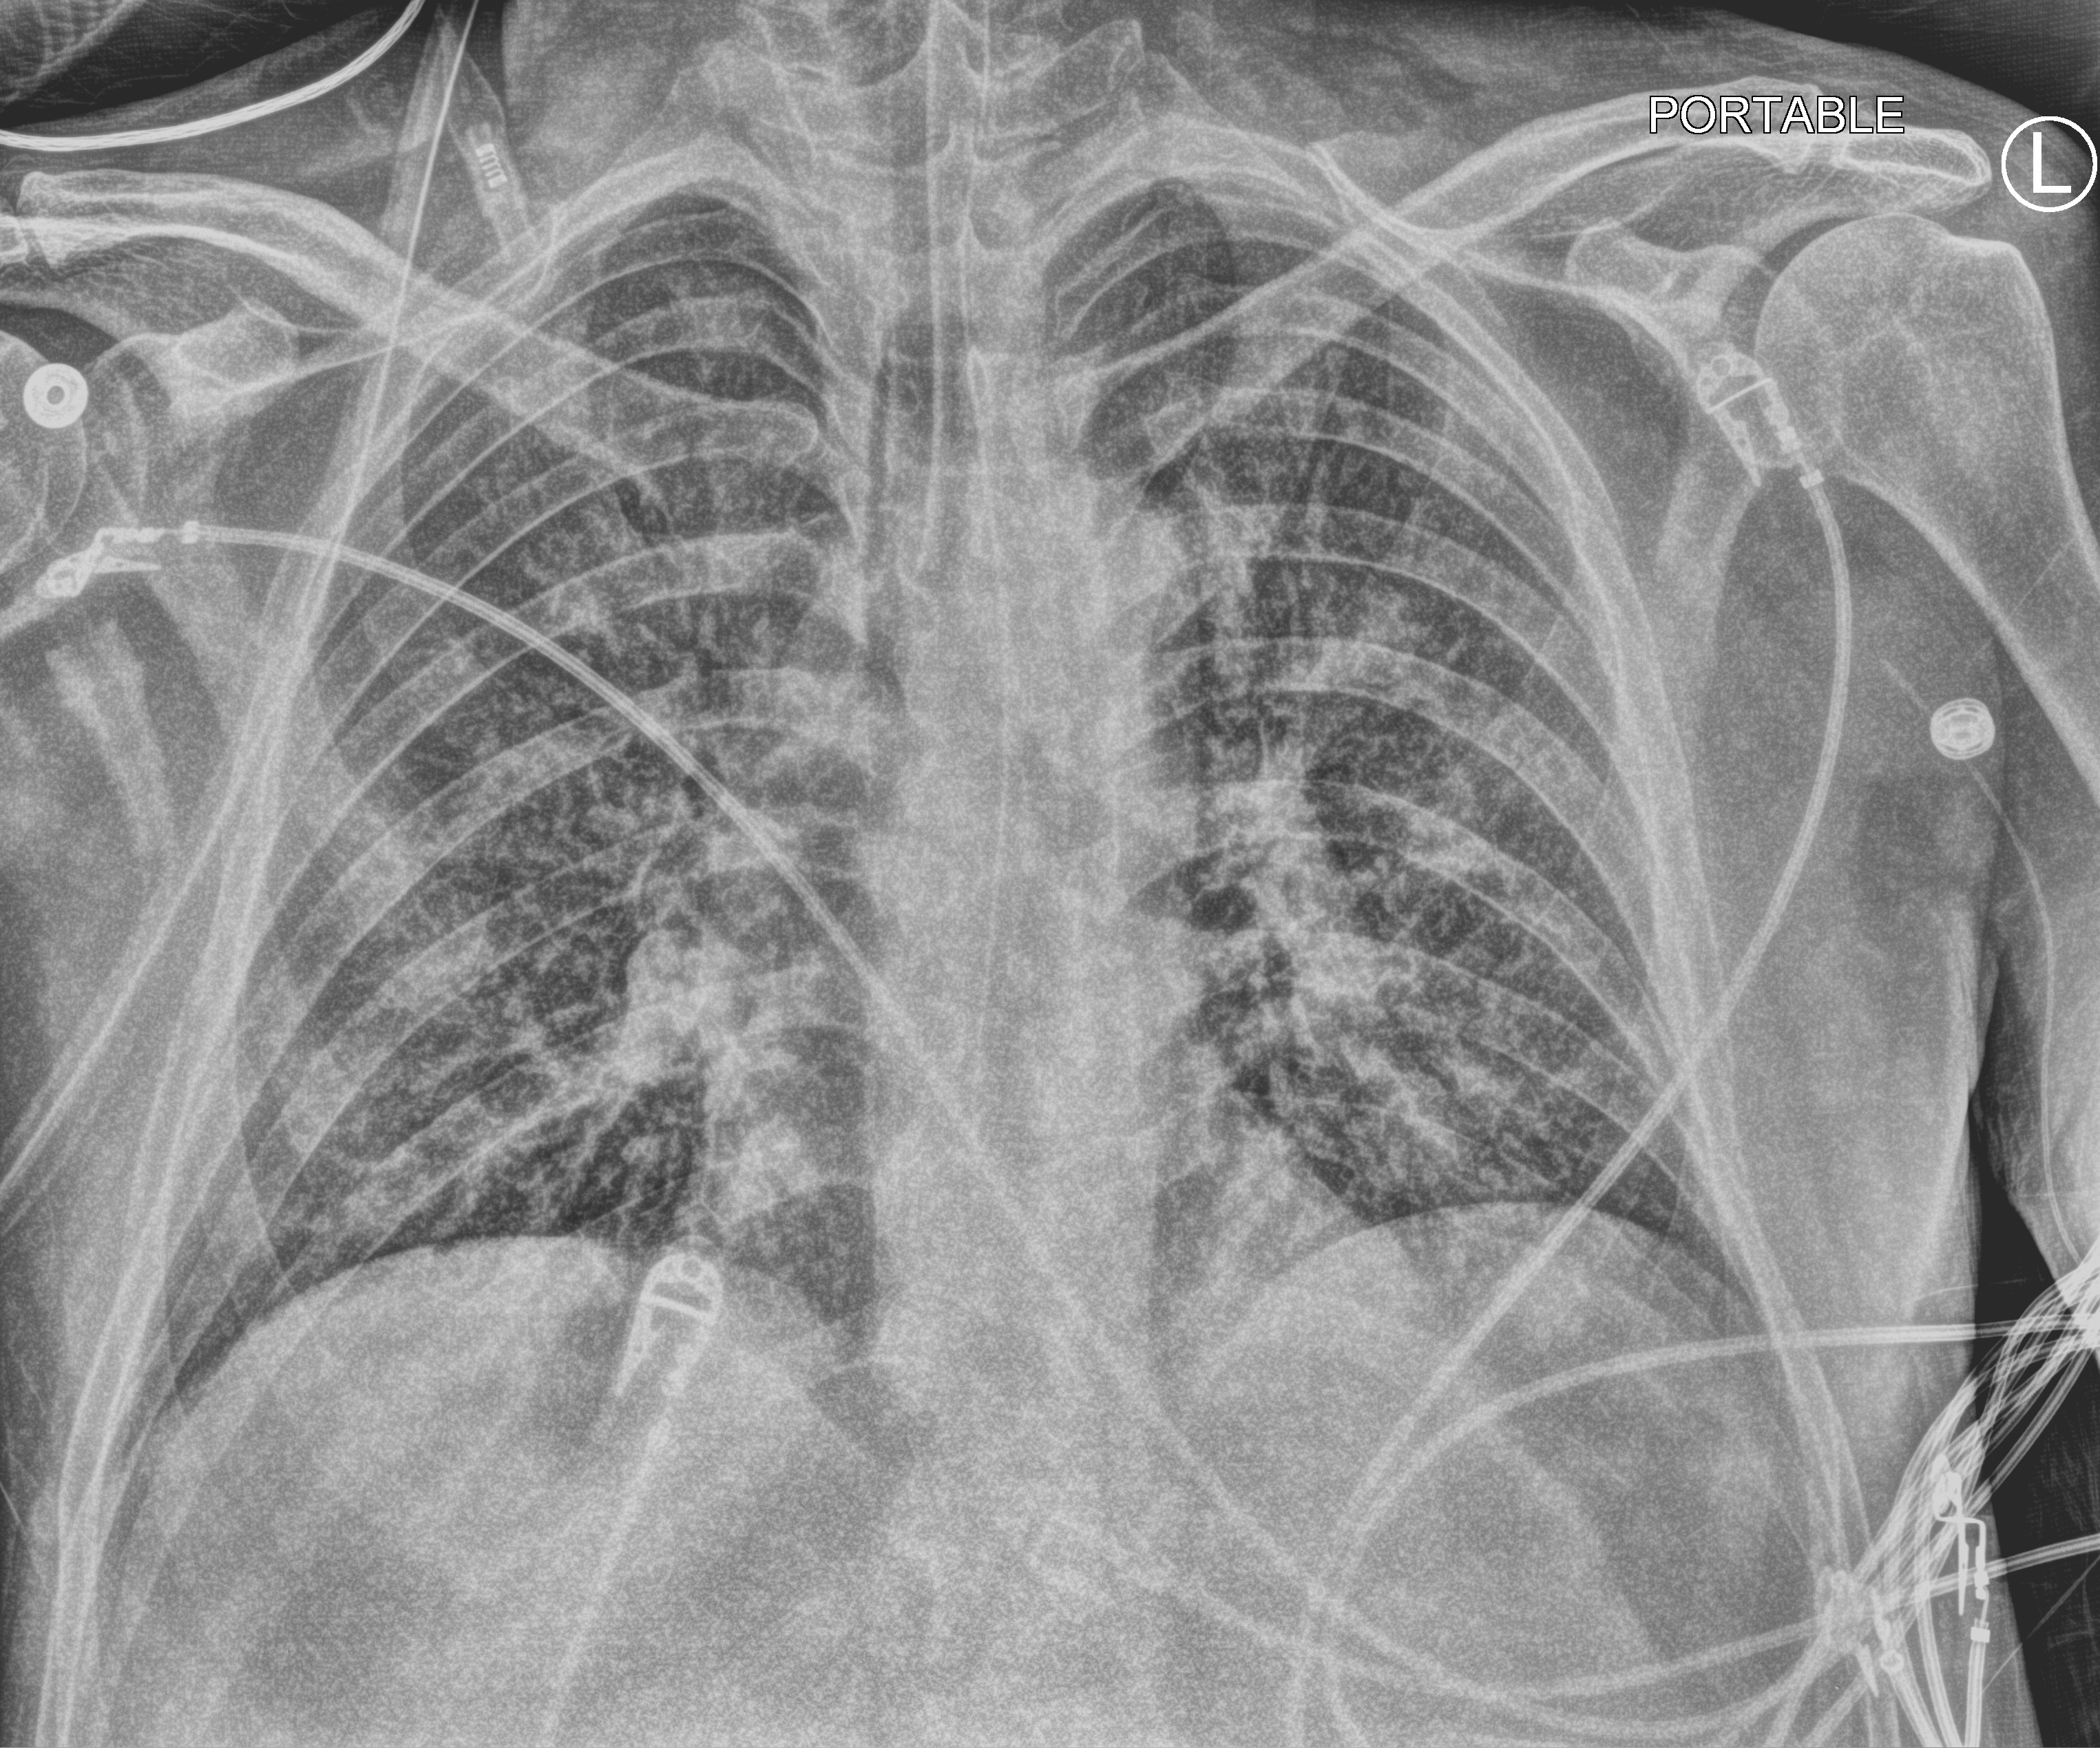
Chest X-ray (portable), anteroposterior (AP) projection. Male patient hospitalised with COVID-19, age 18–59 years.
From the hospital-stay record, not from the radiograph (when in the stay this image was taken is not recorded): admitted to intensive care during this hospital stay: no; mechanically ventilated during this hospital stay: yes.